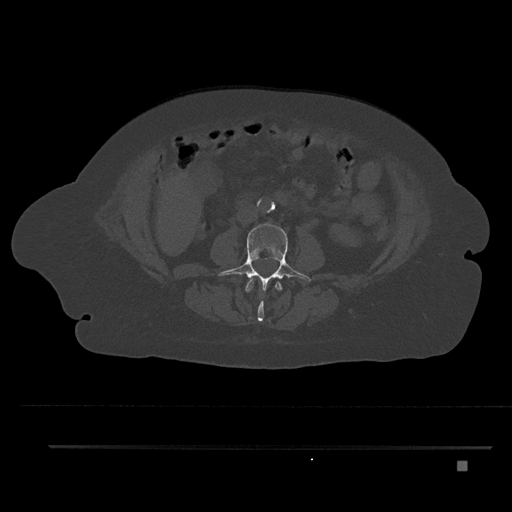
CT including the spine, one axial slice; slice 132 of 797 in the series (ordered by position); bone window (W 1800 / L 400 HU); 512 × 512 image matrix, field of view 437 × 437 mm. Female patient, age 76 years. From the clinical record (not read from this slice): primary cancer: lung.
Outlined on this slice (semi-automatically segmented with operator editing):
- L2 vertebra: box from (x=245, y=279) to (x=282, y=322) px
- L3 vertebra: (x=218, y=223)–(x=311, y=291)